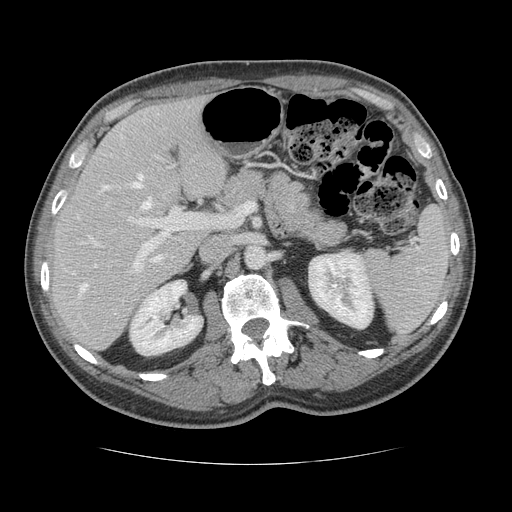
Contrast-enhanced abdominal CT, one axial slice; slice 75 of 134 in the series (ordered by position); 120 kVp; intravenous contrast given; soft-tissue window (W 400 / L 40 HU); 2.5 mm slice thickness; 512 × 512 image matrix, field of view 377 × 377 mm. Male patient, age 68 years. From the clinical record (not read from this slice): diagnosis: colorectal cancer liver metastases, imaged before liver resection; multiple liver metastases: yes; largest metastasis: 2.2 cm; disease in both lobes: no.
Structures marked on this image (expert manual segmentation):
- hepatic veins: box from (x=73, y=174) to (x=151, y=293) px
- liver: (x=51, y=94)–(x=227, y=350)
- planned liver remnant (the part of the liver to remain after resection): (x=51, y=94)–(x=227, y=336)
- portal vein (with intrahepatic branches): (x=128, y=166)–(x=197, y=270)